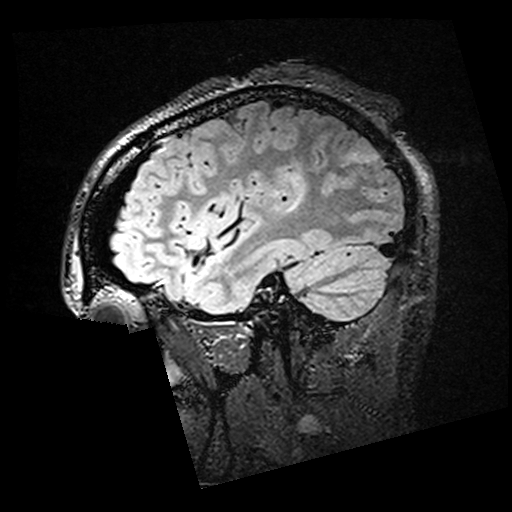
Brain MRI from a brain-tumour surgery series, one sagittal slice. Position 48 of 176 along the scan axis. T2 FLAIR. 1 mm slice thickness. 512 × 512 image matrix, field of view 250 × 250 mm. From the clinical record (not read from this slice): histopathology: Oligodendroglioma; WHO grade: 2.
Outlined on this slice (expert manual segmentation):
- residual tumour: box from (x=285, y=173) to (x=304, y=190) px